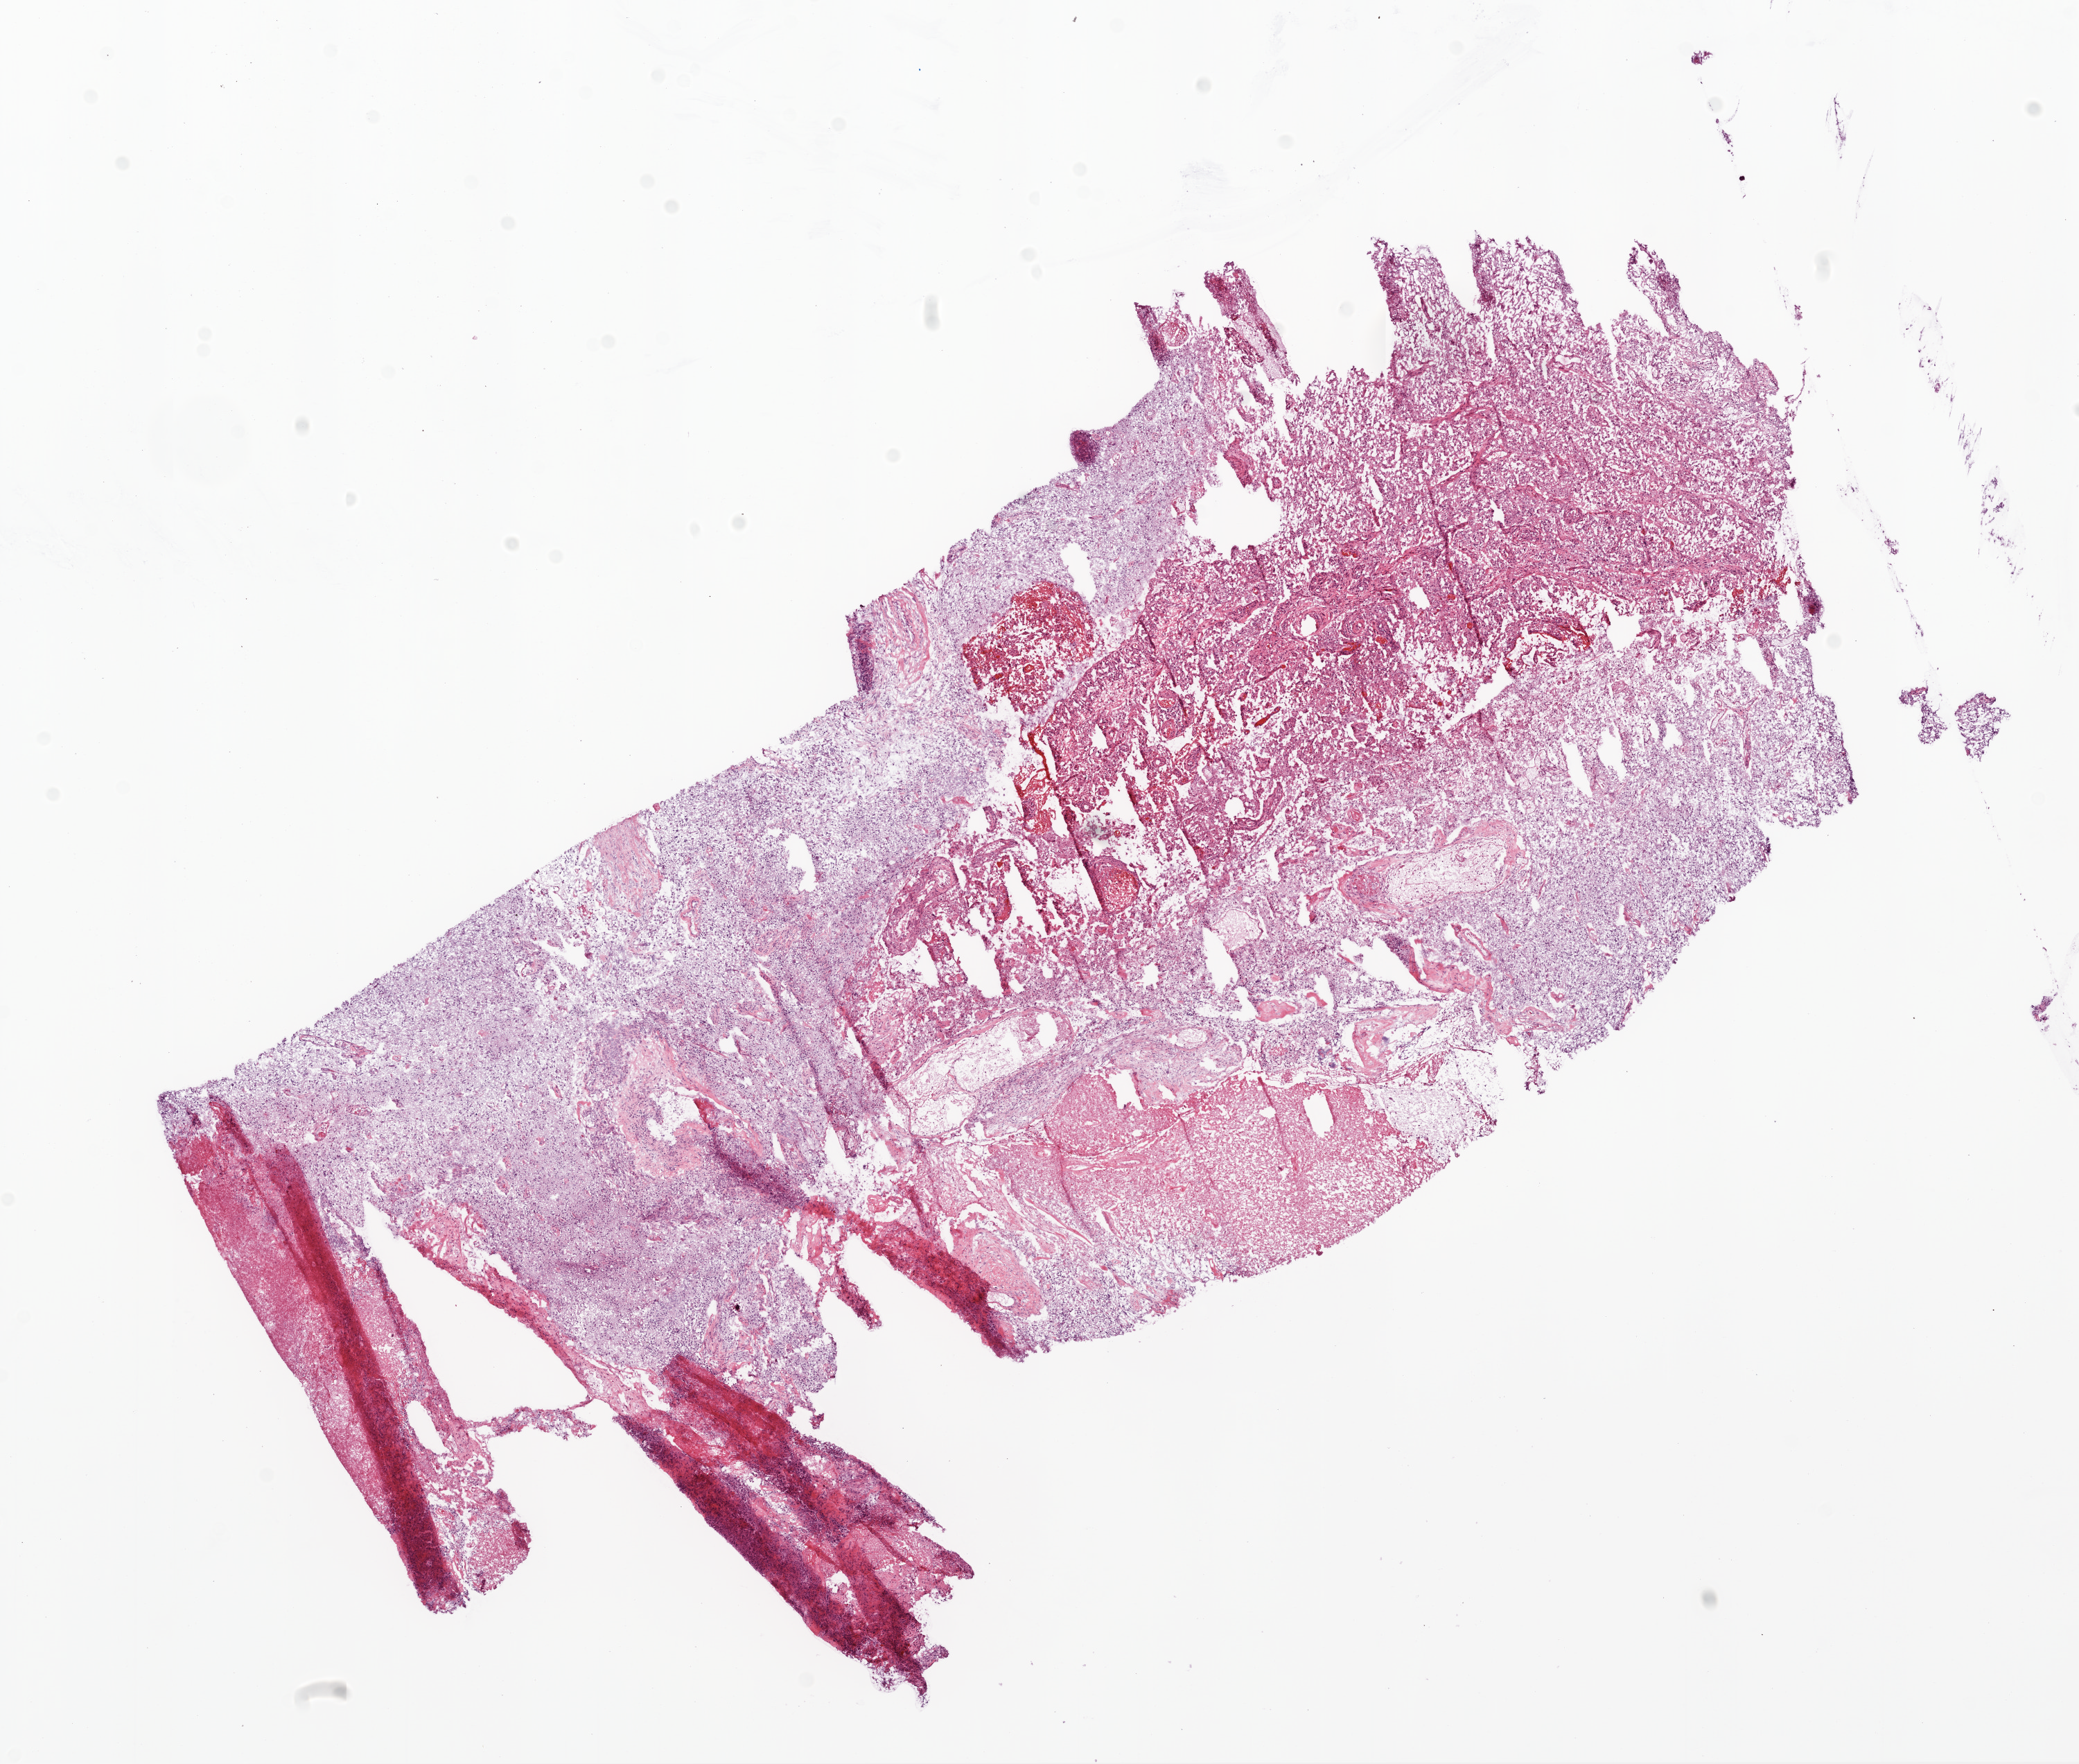
Digitized H&E tissue section (whole slide) — shown as a low-resolution overview of the whole scanned area (about 12.0 x 10.2 mm). Frozen section from the top of the tissue portion. Sample: primary tumour, brain. Patient: male, age at initial diagnosis 68 years. Composition of this section per pathologist review: tumour cells 75%, tumour nuclei 85%, normal cells 0%, stromal cells 5%, necrosis 20%.
Diagnosis: Glioblastoma (temporal lobe).